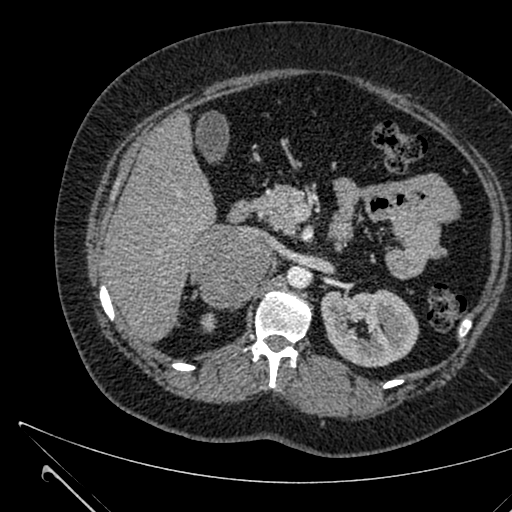
Contrast-enhanced abdominal CT, one axial slice; 120 kVp; soft-tissue window (W 400 / L 40 HU); 512 × 512 image matrix. Female patient, age 36 years. From the clinical record (not read from this slice): diagnosis: adrenocortical carcinoma; tumour side: right adrenal; tumour size at pathology: 10 cm; Ki-67 index: 20 %; stage (as recorded): 4.
Annotated regions visible in this slice (semi-automatically segmented with operator editing):
- mass: bounding box (x1, y1, x2, y2) in pixels: (192, 225, 267, 305)